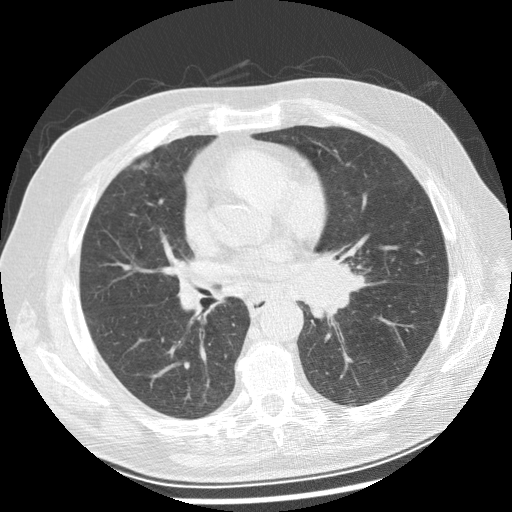
Low-dose screening chest CT, one axial slice; slice 132 of 250 in the series (ordered by position); lung window (W 1500 / L -600 HU); 512 × 512 image matrix, field of view 360 × 360 mm.
Structures marked on this image (manually delineated by an expert):
- lesion 1 (tumor, left main bronchus): bounding box <304,259,367,320> (left, top, right, bottom; pixels)